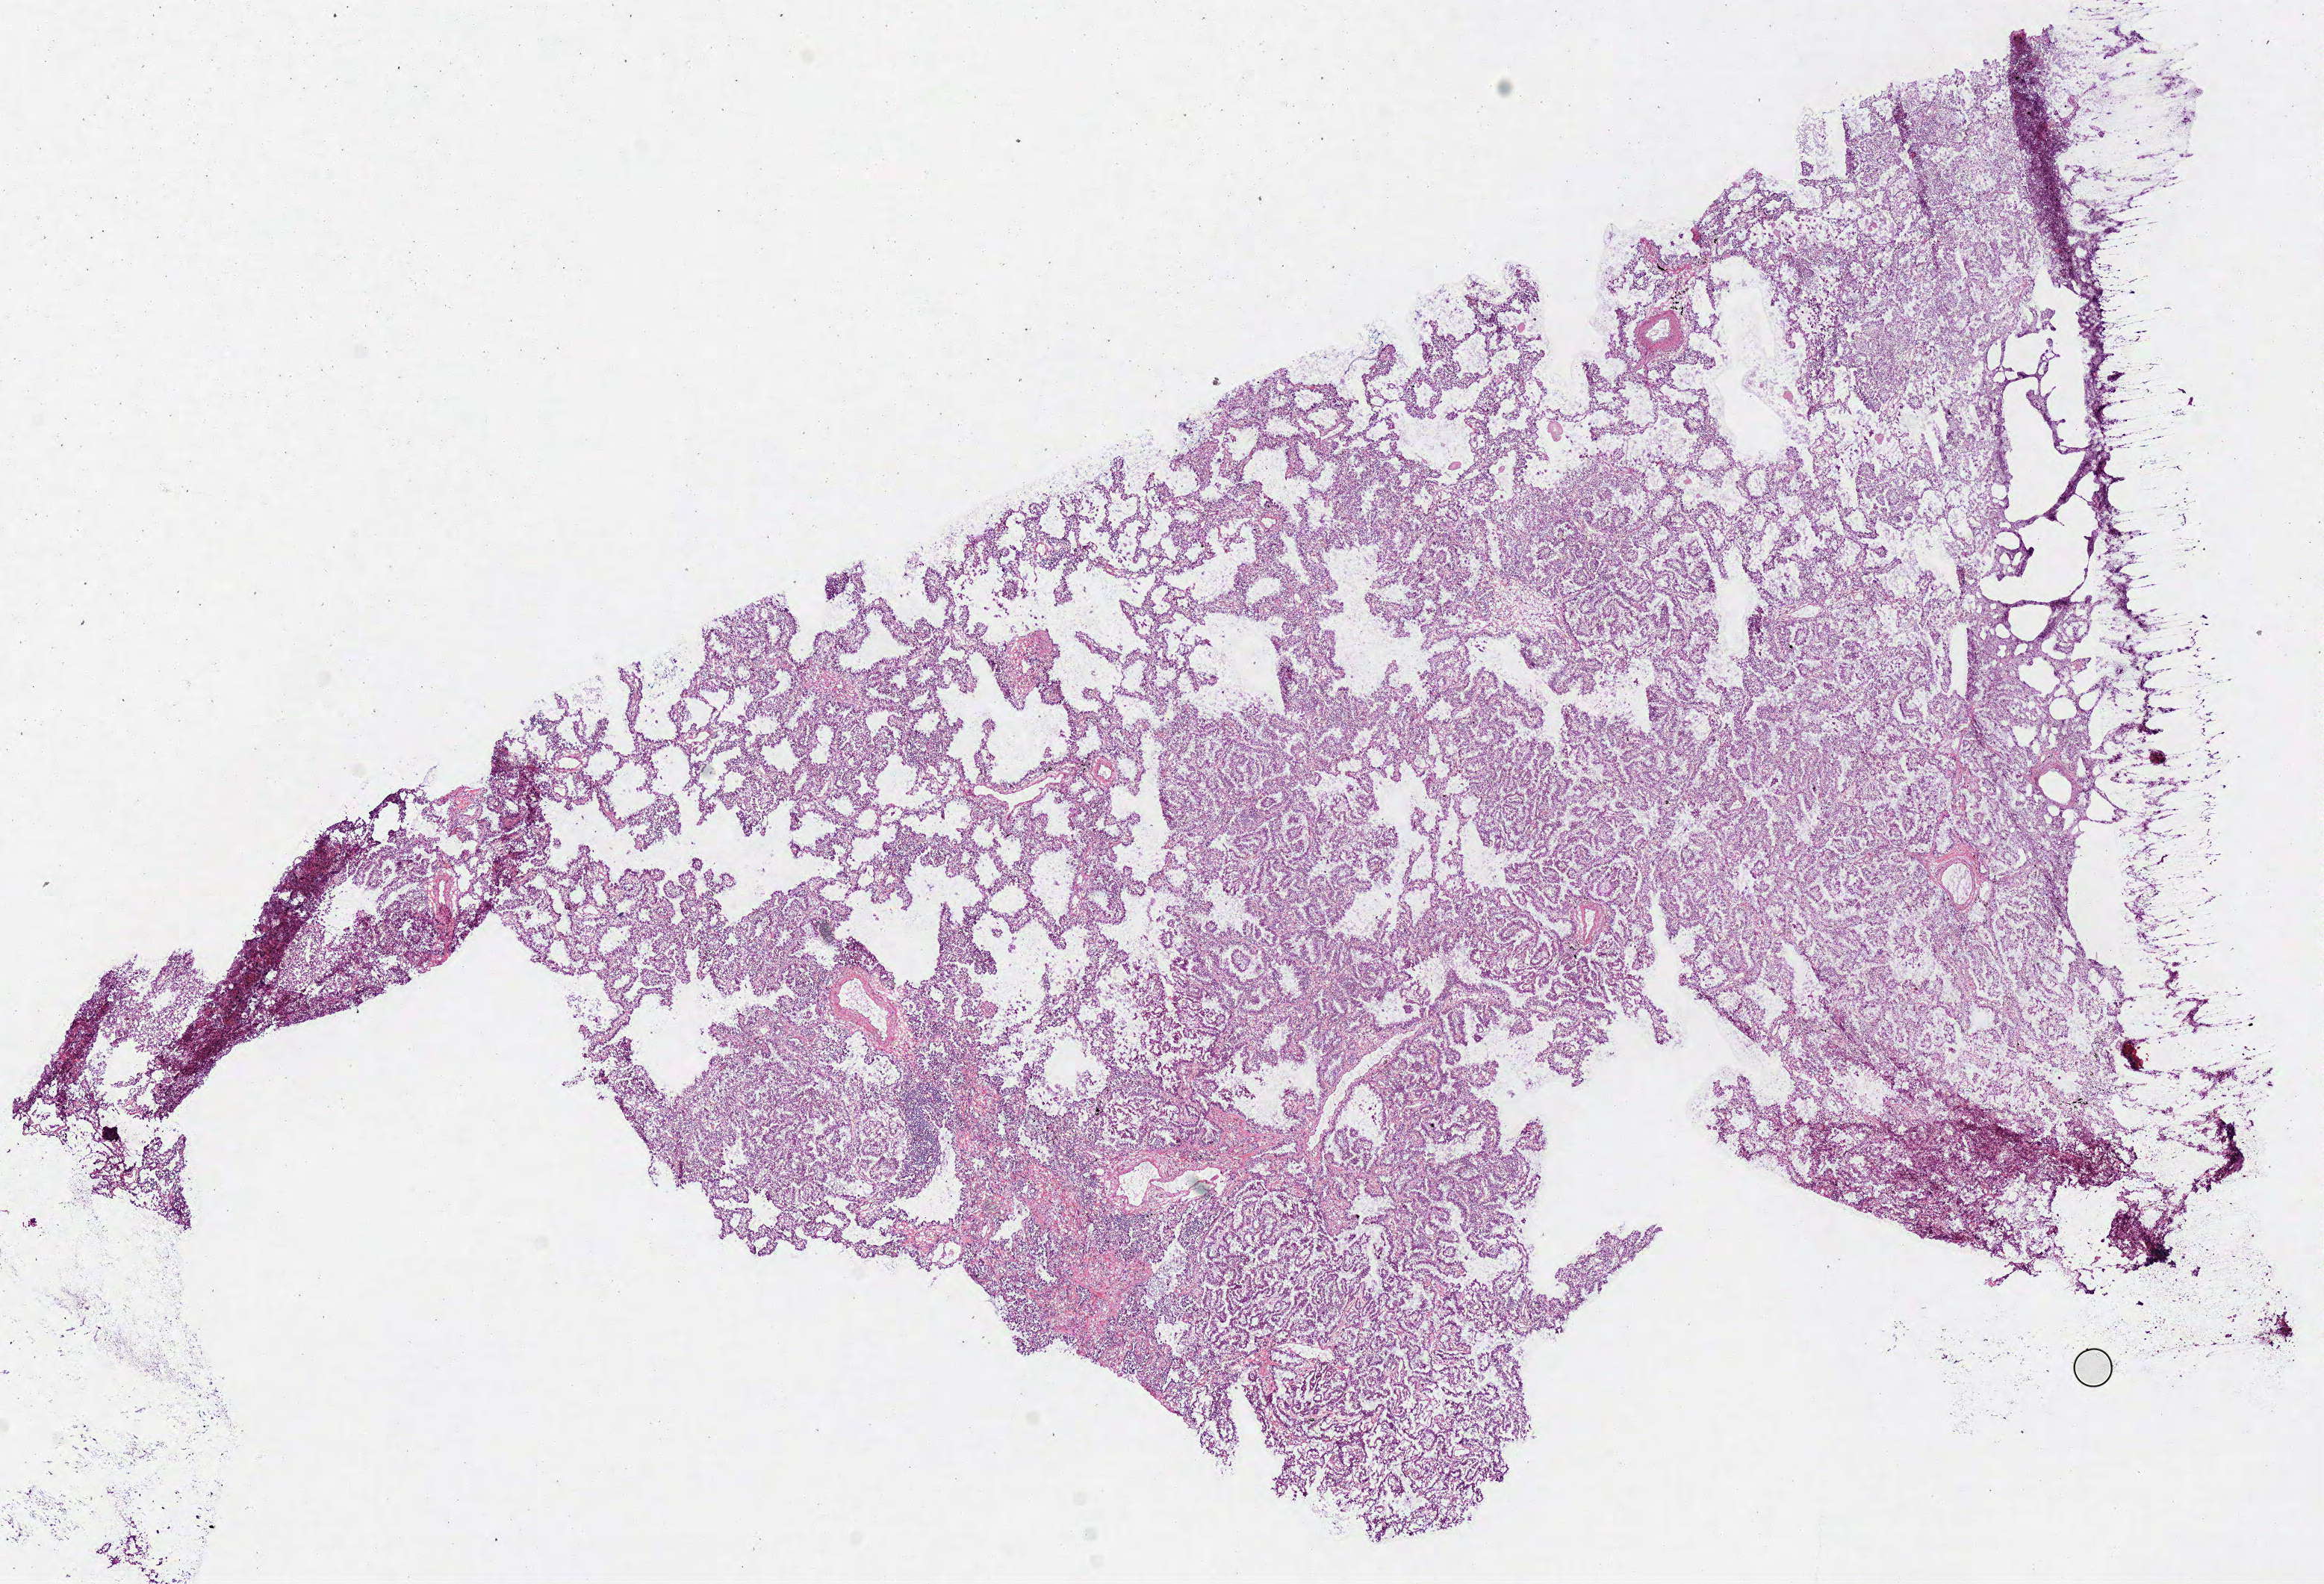
Whole-slide histology image, H&E-stained — a low-resolution overview of the entire scanned area, about 12.2 x 8.3 mm (acquisition: 40x scan); frozen section from the bottom of the tissue portion; sample: primary tumour, lung. Patient: female, age at initial diagnosis 60 years. Composition of this section per pathologist review: tumour cells 100%, tumour nuclei 90%, normal cells 0%, stromal cells 0%, necrosis 0%. Infiltration values recorded for this section: lymphocyte infiltration 5%, monocyte infiltration 2%, neutrophil infiltration 0%.
• TNM: T1 N0 MX
• laterality: right
• AJCC pathologic stage: IA (6th edition)
• pathologic diagnosis: Adenocarcinoma, NOS (upper lobe, lung)